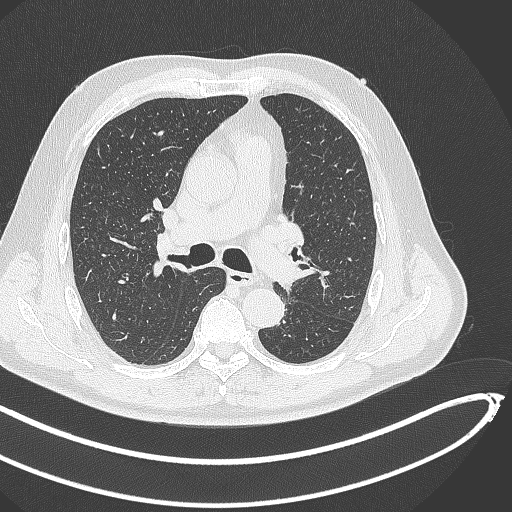
Chest CT, one axial slice. Reconstruction kernel B70f. 120 kVp. Lung window (W 1500 / L -600 HU). 512 × 512 image matrix, field of view 400 × 400 mm. Male patient, age 64 years. Case-level facts recorded for this patient, not image findings: clinical TNM (as recorded): T1c N0 M0; histopathological grade: G2.
Structures marked on this image (bounding box drawn by a radiologist):
- lung tumour (recorded histology: squamous cell carcinoma): bounding box (x1, y1, x2, y2) in pixels: (270, 261, 306, 294)